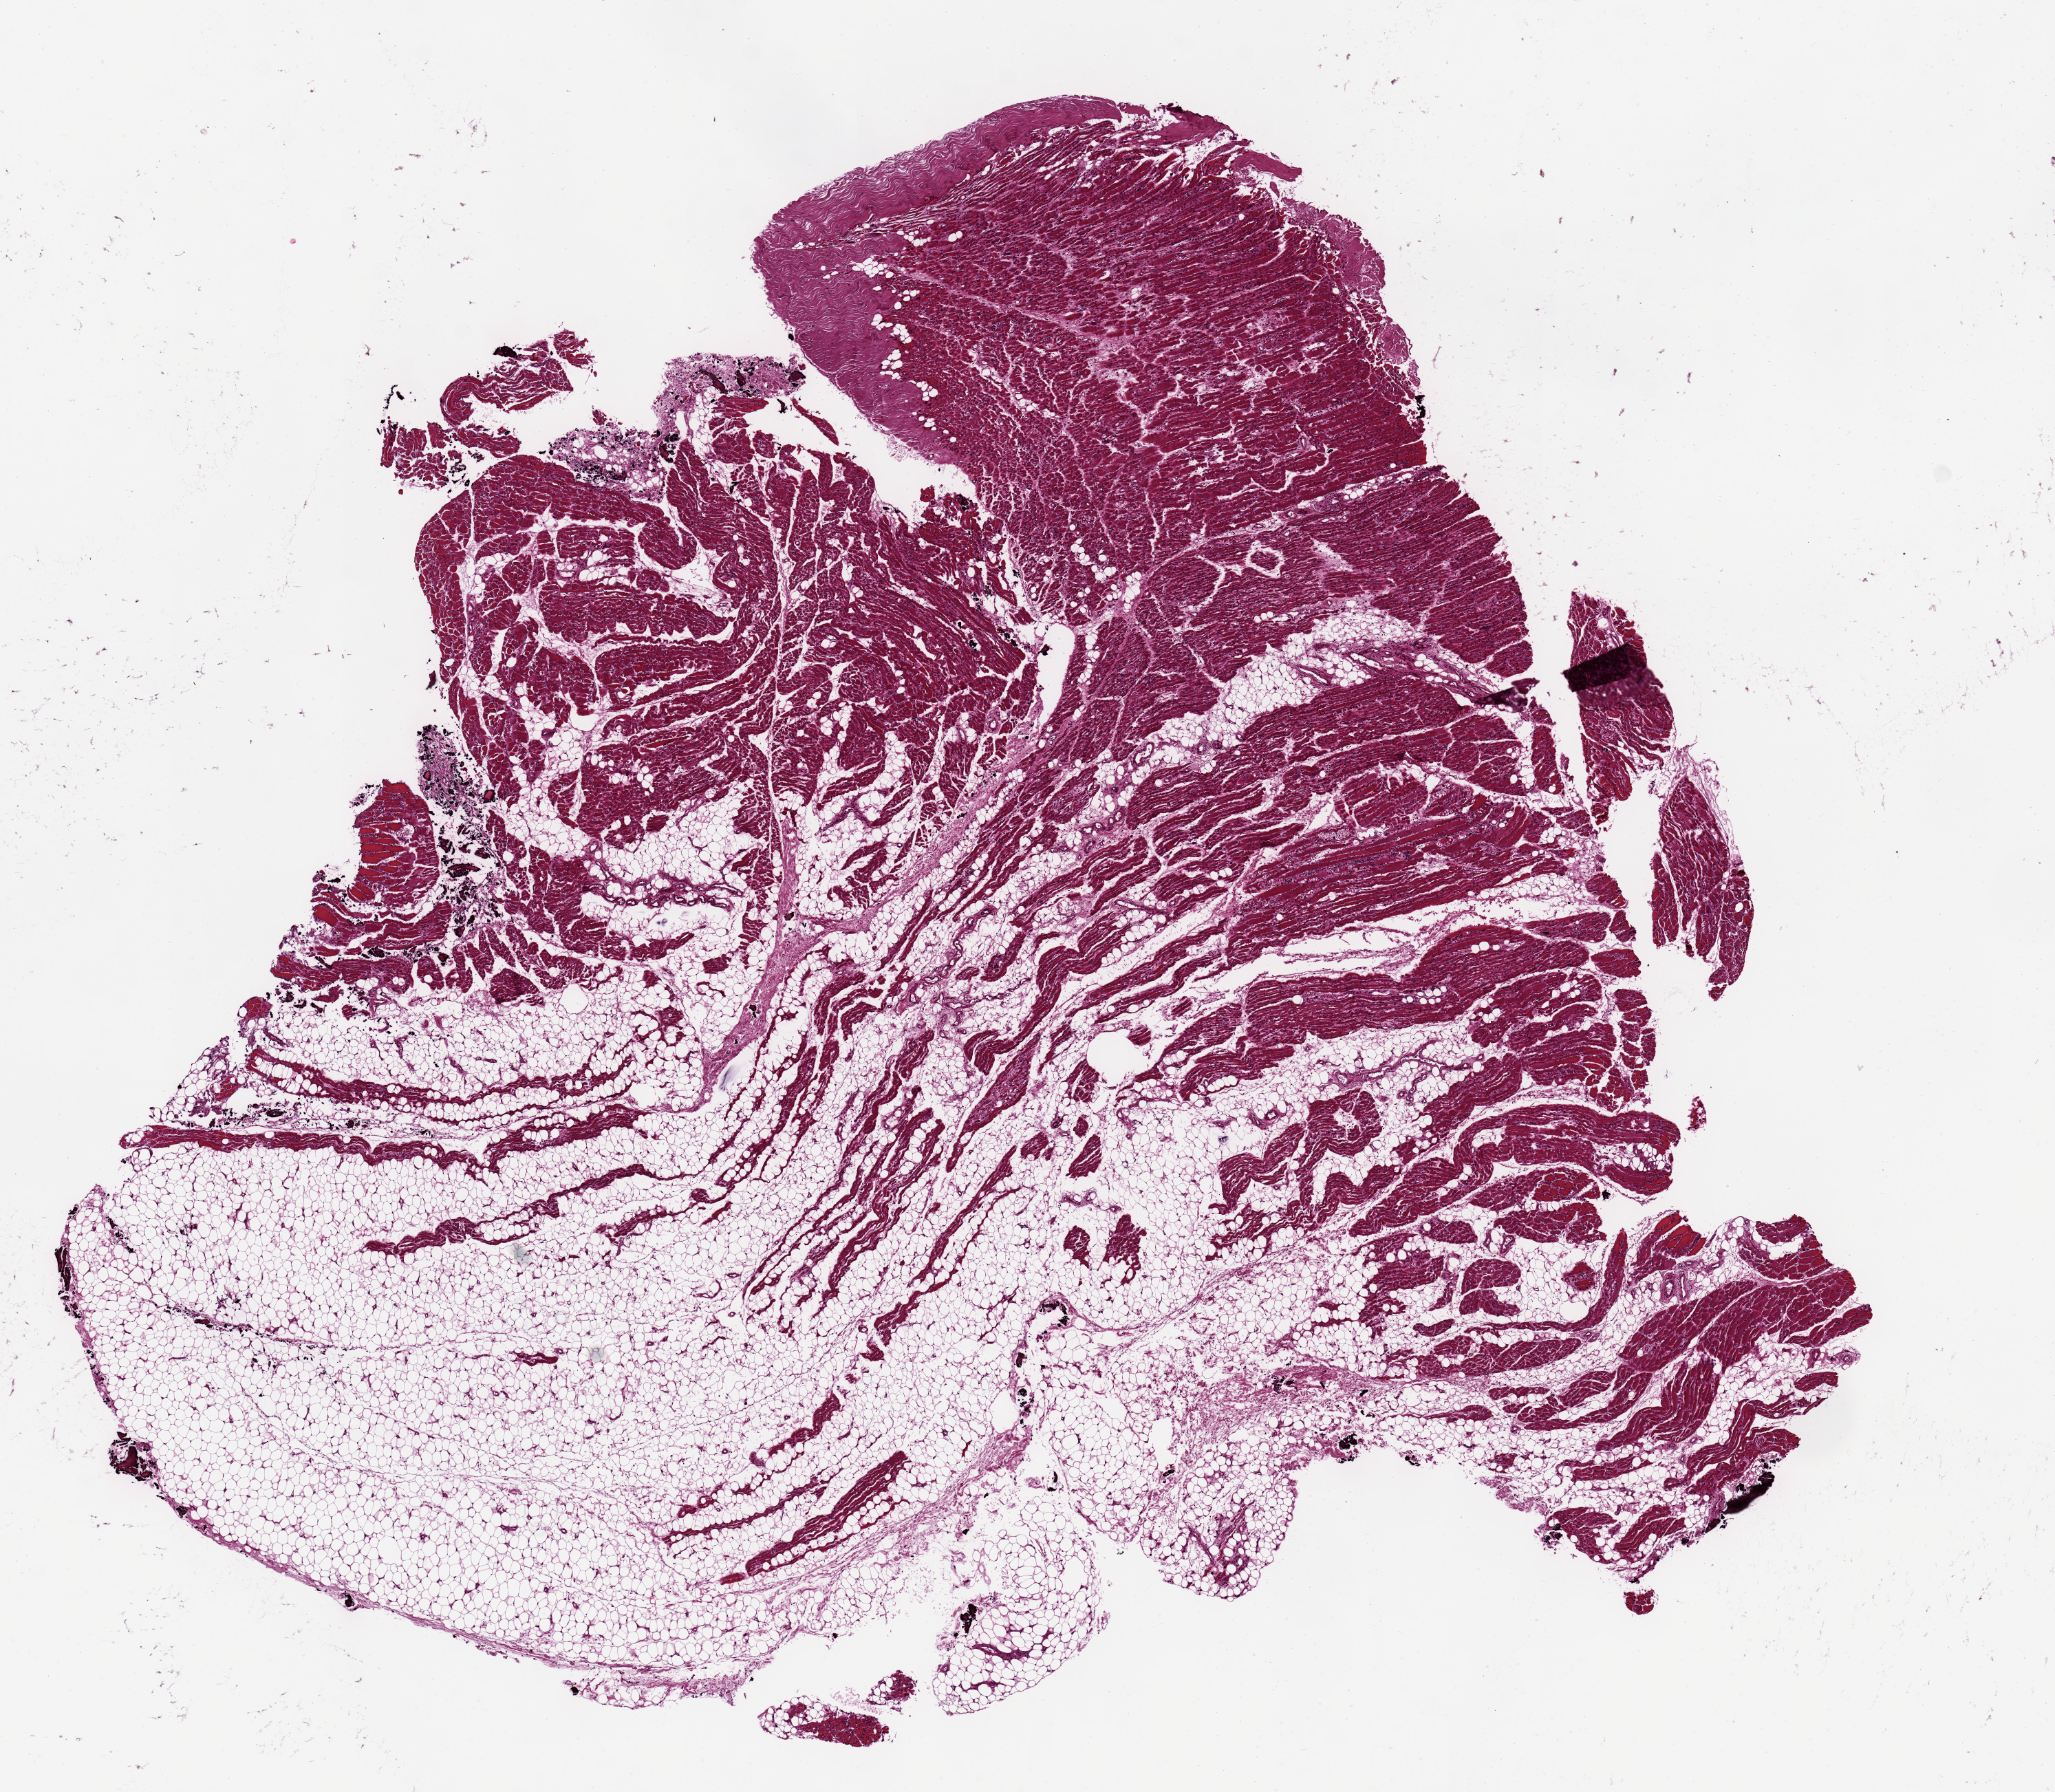
Digitized haematoxylin and eosin-stained section — a low-resolution overview of the entire scanned area, about 11.8 x 10.3 mm; PAXgene-fixed, paraffin-embedded tissue; section of skeletal muscle (target tissue); donor tissue sample. Female donor.
- reviewer comment on this tissue sample: Appear atrophic; 50% adipose